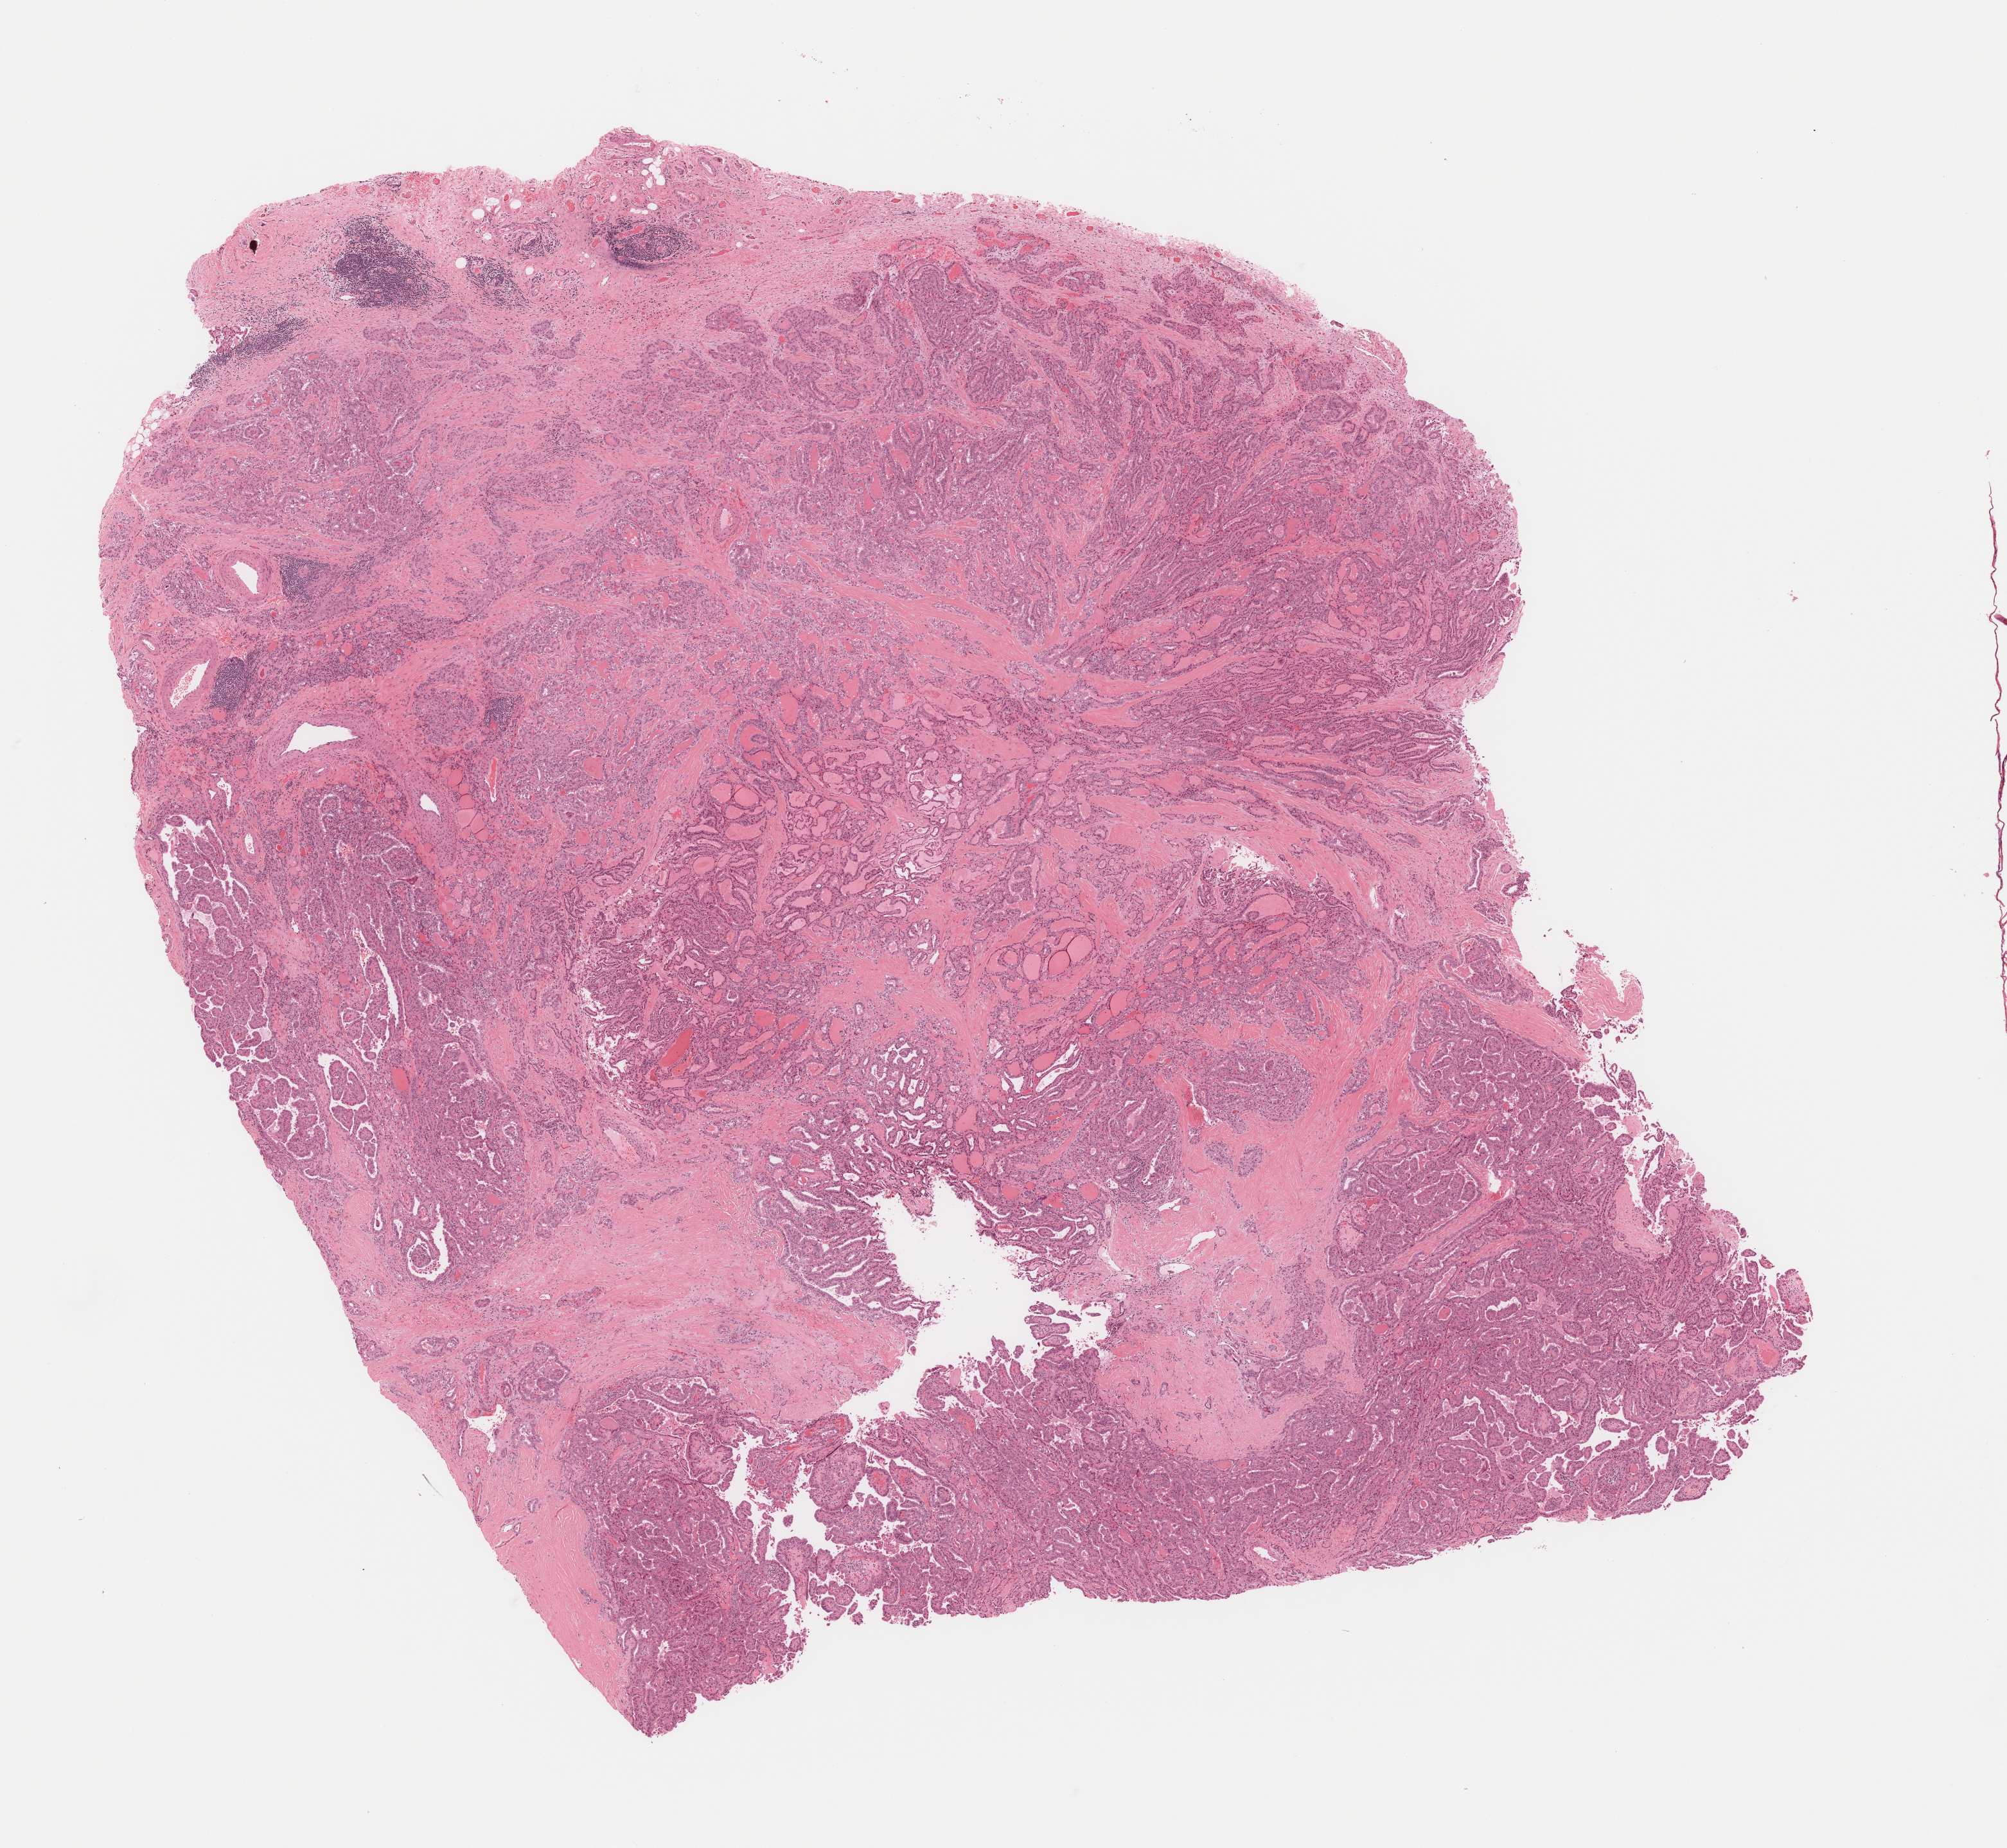
Whole-slide histology image, H&E-stained, whole scanned area (about 12.6 x 11.6 mm) shown as a low-resolution overview; formalin-fixed paraffin-embedded (FFPE) diagnostic section; sample: primary tumour, thyroid. Female patient; age at initial diagnosis 52 years.
Pathologic diagnosis: Papillary adenocarcinoma, NOS (thyroid gland). Lymph nodes positive (case pathology): 0 of 1 examined. AJCC pathologic stage: III.